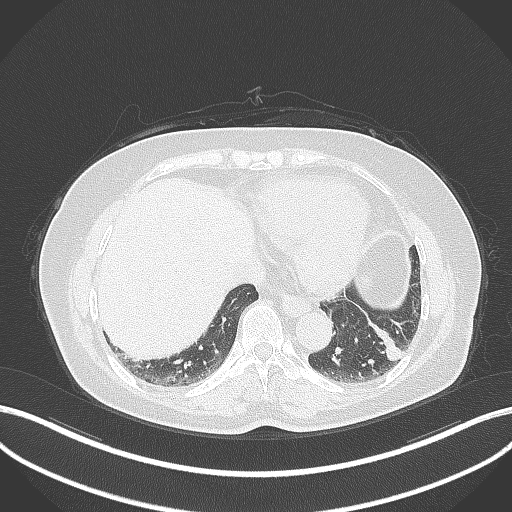
Chest CT, one axial slice; position 108 of 311 along the scan axis; reconstruction kernel B70f; lung window (W 1500 / L -600 HU); 1 mm slice thickness; 512 × 512 image matrix. Patient: female, 59 years. From the clinical record (not read from this slice): clinical TNM (as recorded): T2a N0 M0; histopathological grade: G2-3.
Annotated regions visible in this slice (rectangle marked by the reading radiologist):
- lung tumour (recorded histology: adenocarcinoma): bounding box [x1, y1, x2, y2] px = [359, 310, 406, 366]